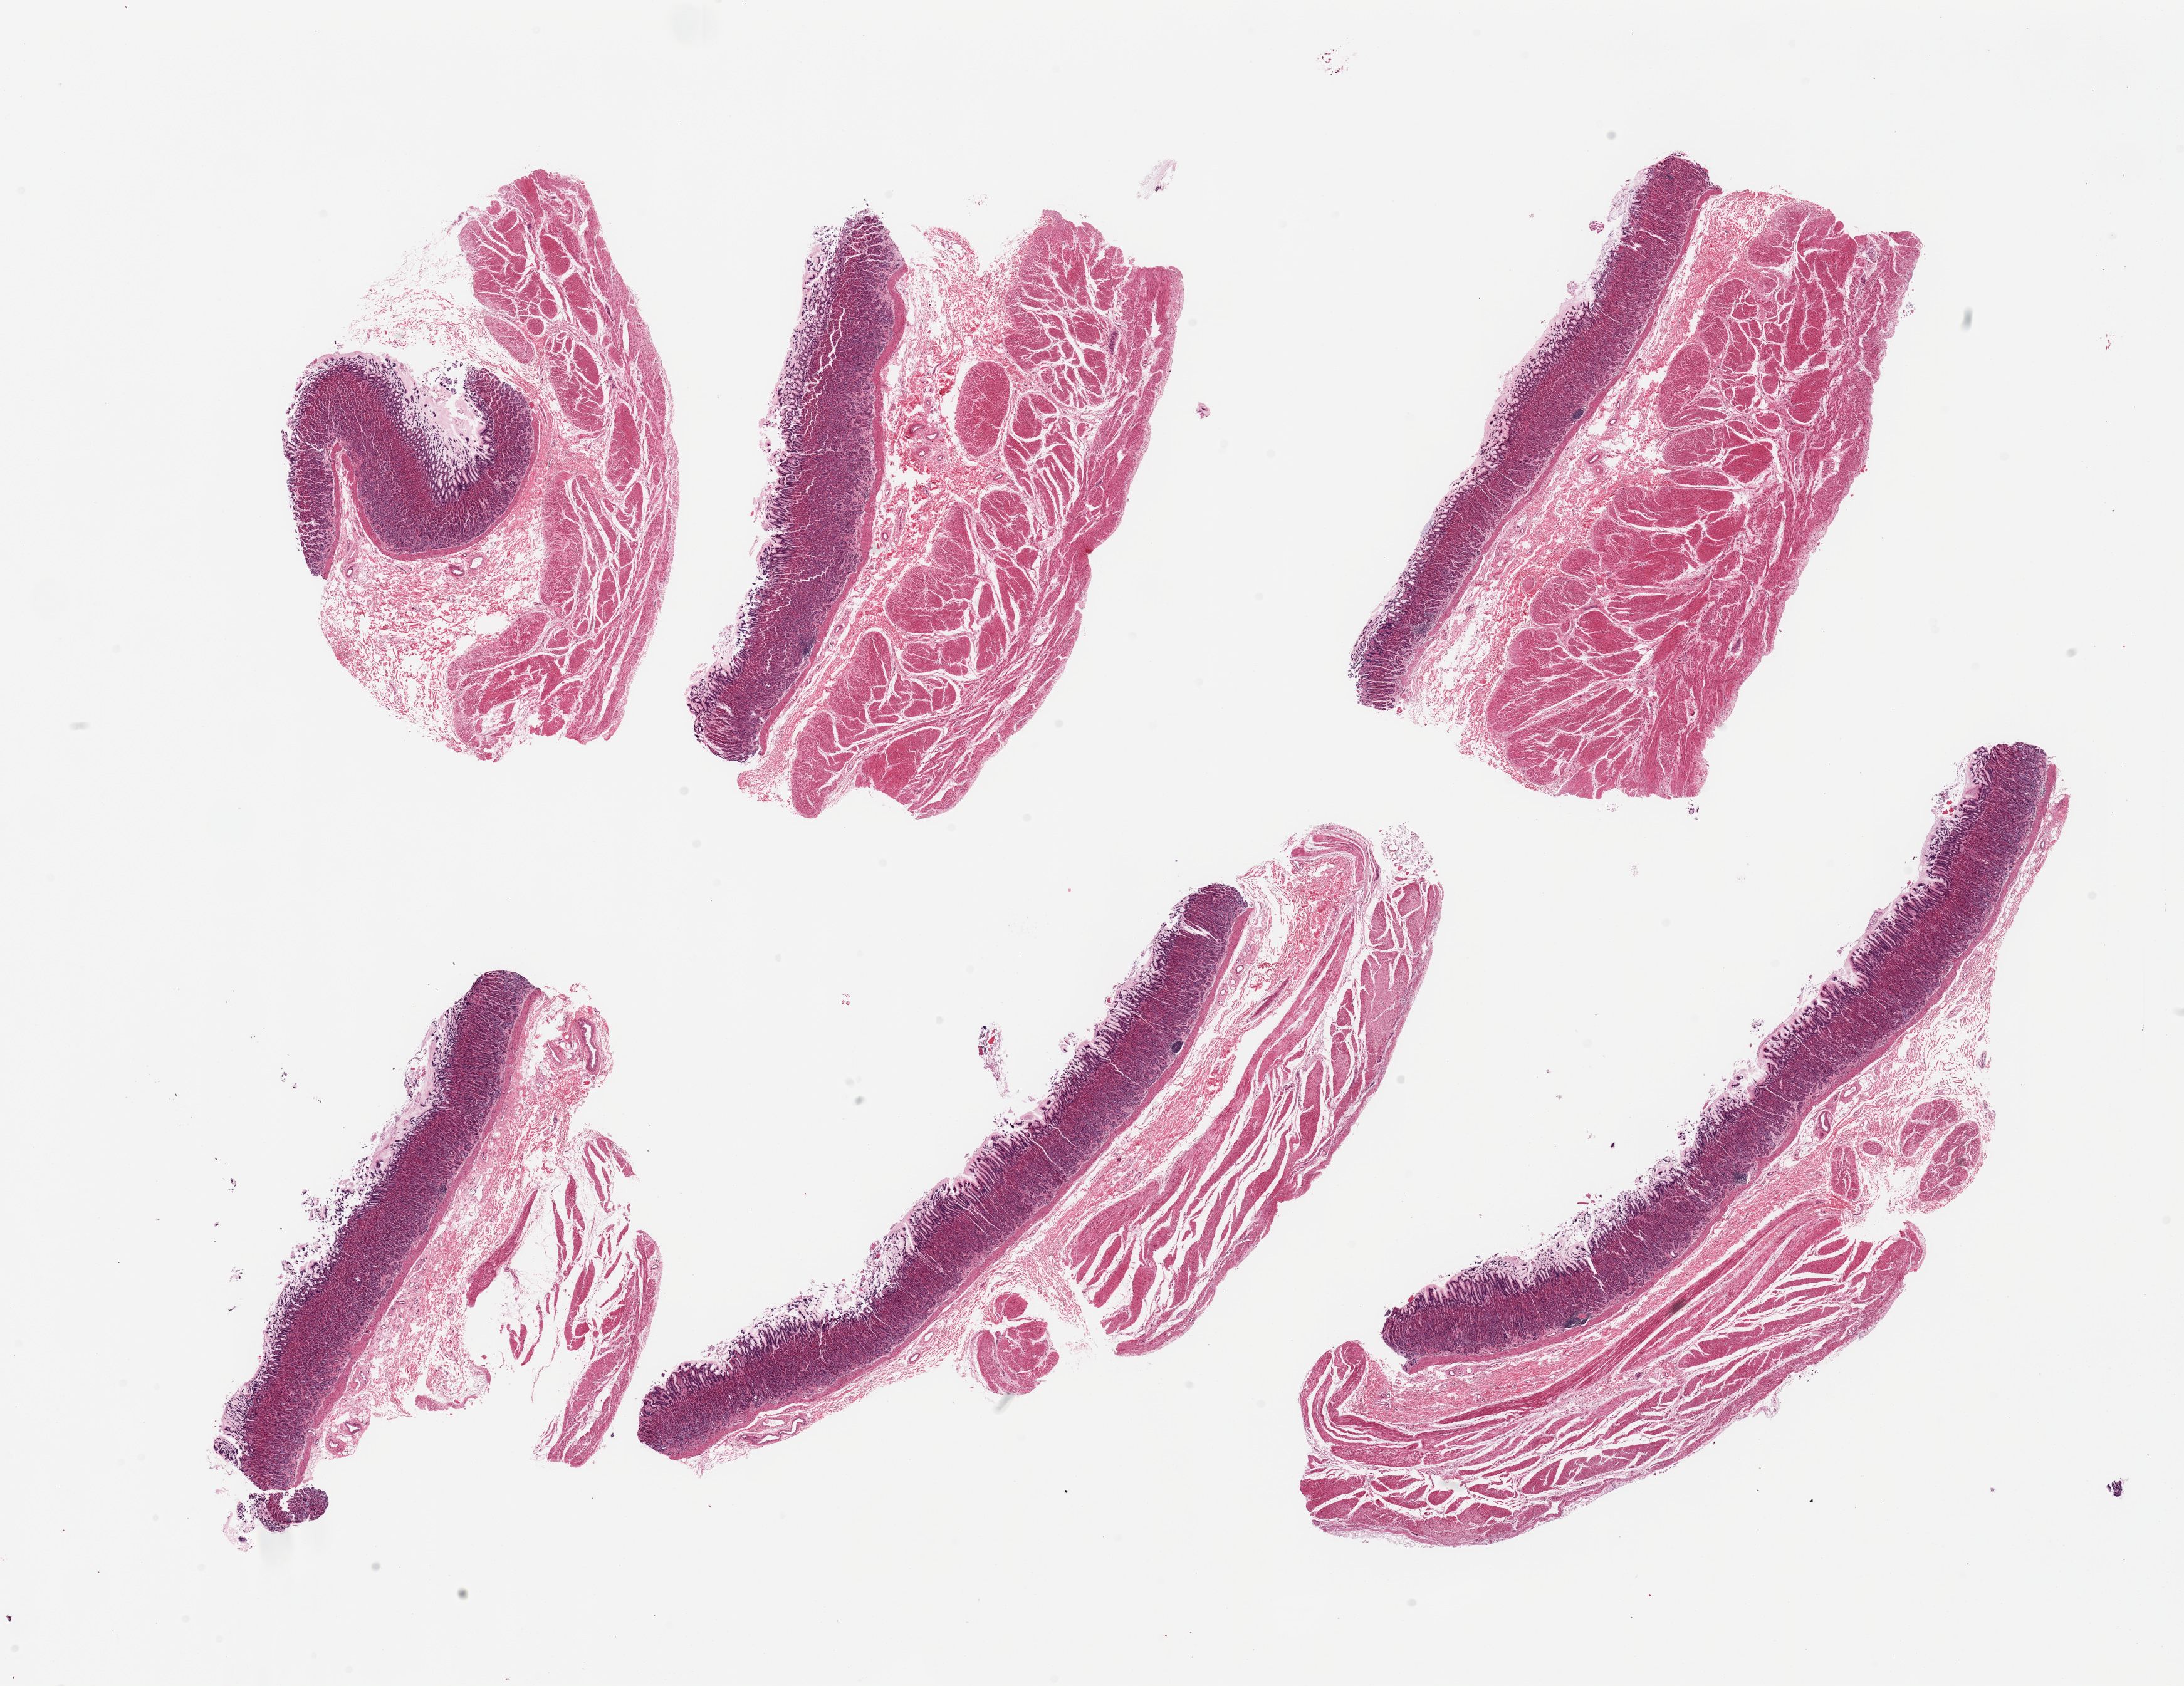
Whole-slide image, hematoxylin and eosin (H&E) stain, brightfield — a low-resolution overview of the entire scanned area, about 27.6 x 21.3 mm (from a 20x scan), PAXgene-fixed, paraffin-embedded tissue, section of stomach (target tissue), tissue donor sample. Donor sex: female.
Pathologist's review note for this sample: 6 pieces; full thickness; well preserved mucosa except for superficial sloughing.